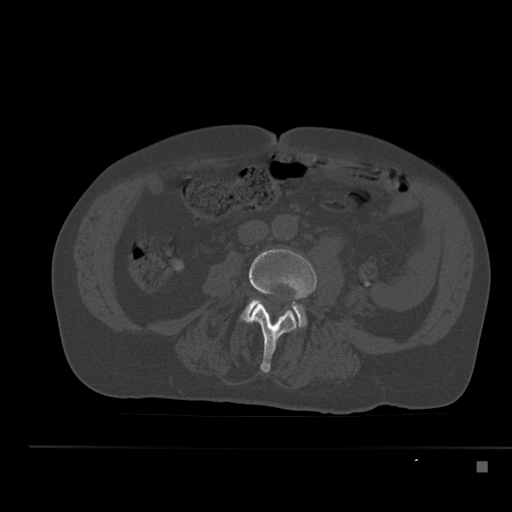
CT including the spine, one axial slice. Bone window (W 1800 / L 400 HU). 512 × 512 image matrix, field of view 408 × 408 mm. Patient: male, 70 years. From the clinical record (not read from this slice): primary cancer: renal.
Annotated regions visible in this slice (semi-automatically segmented with operator editing):
- L3 vertebra: box from (x=249, y=249) to (x=317, y=373) px
- L4 vertebra: (x=241, y=301)–(x=306, y=327)